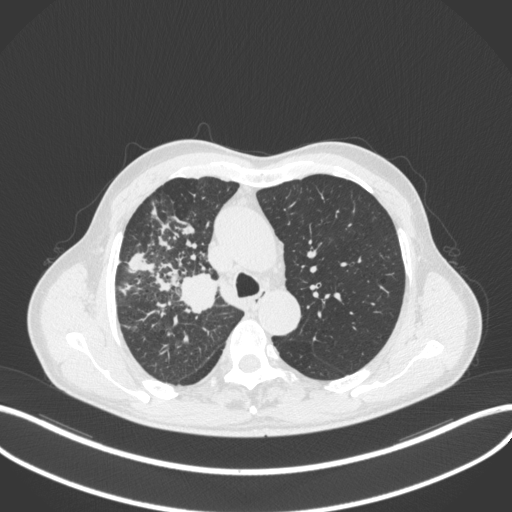
Chest CT, one axial slice. Slice 340 of 490 in the series (ordered by position). Reconstruction kernel B31f. 120 kVp. Lung window (W 1500 / L -600 HU). 1 mm slice thickness. 512 × 512 image matrix. Patient: male, 69 years. From the clinical record (not read from this slice): clinical TNM (as recorded): T2a N0 M0.
Outlined on this slice (bounding box drawn by a radiologist):
- lung tumour (recorded histology: adenocarcinoma): bounding box [x1, y1, x2, y2] px = [176, 272, 219, 314]